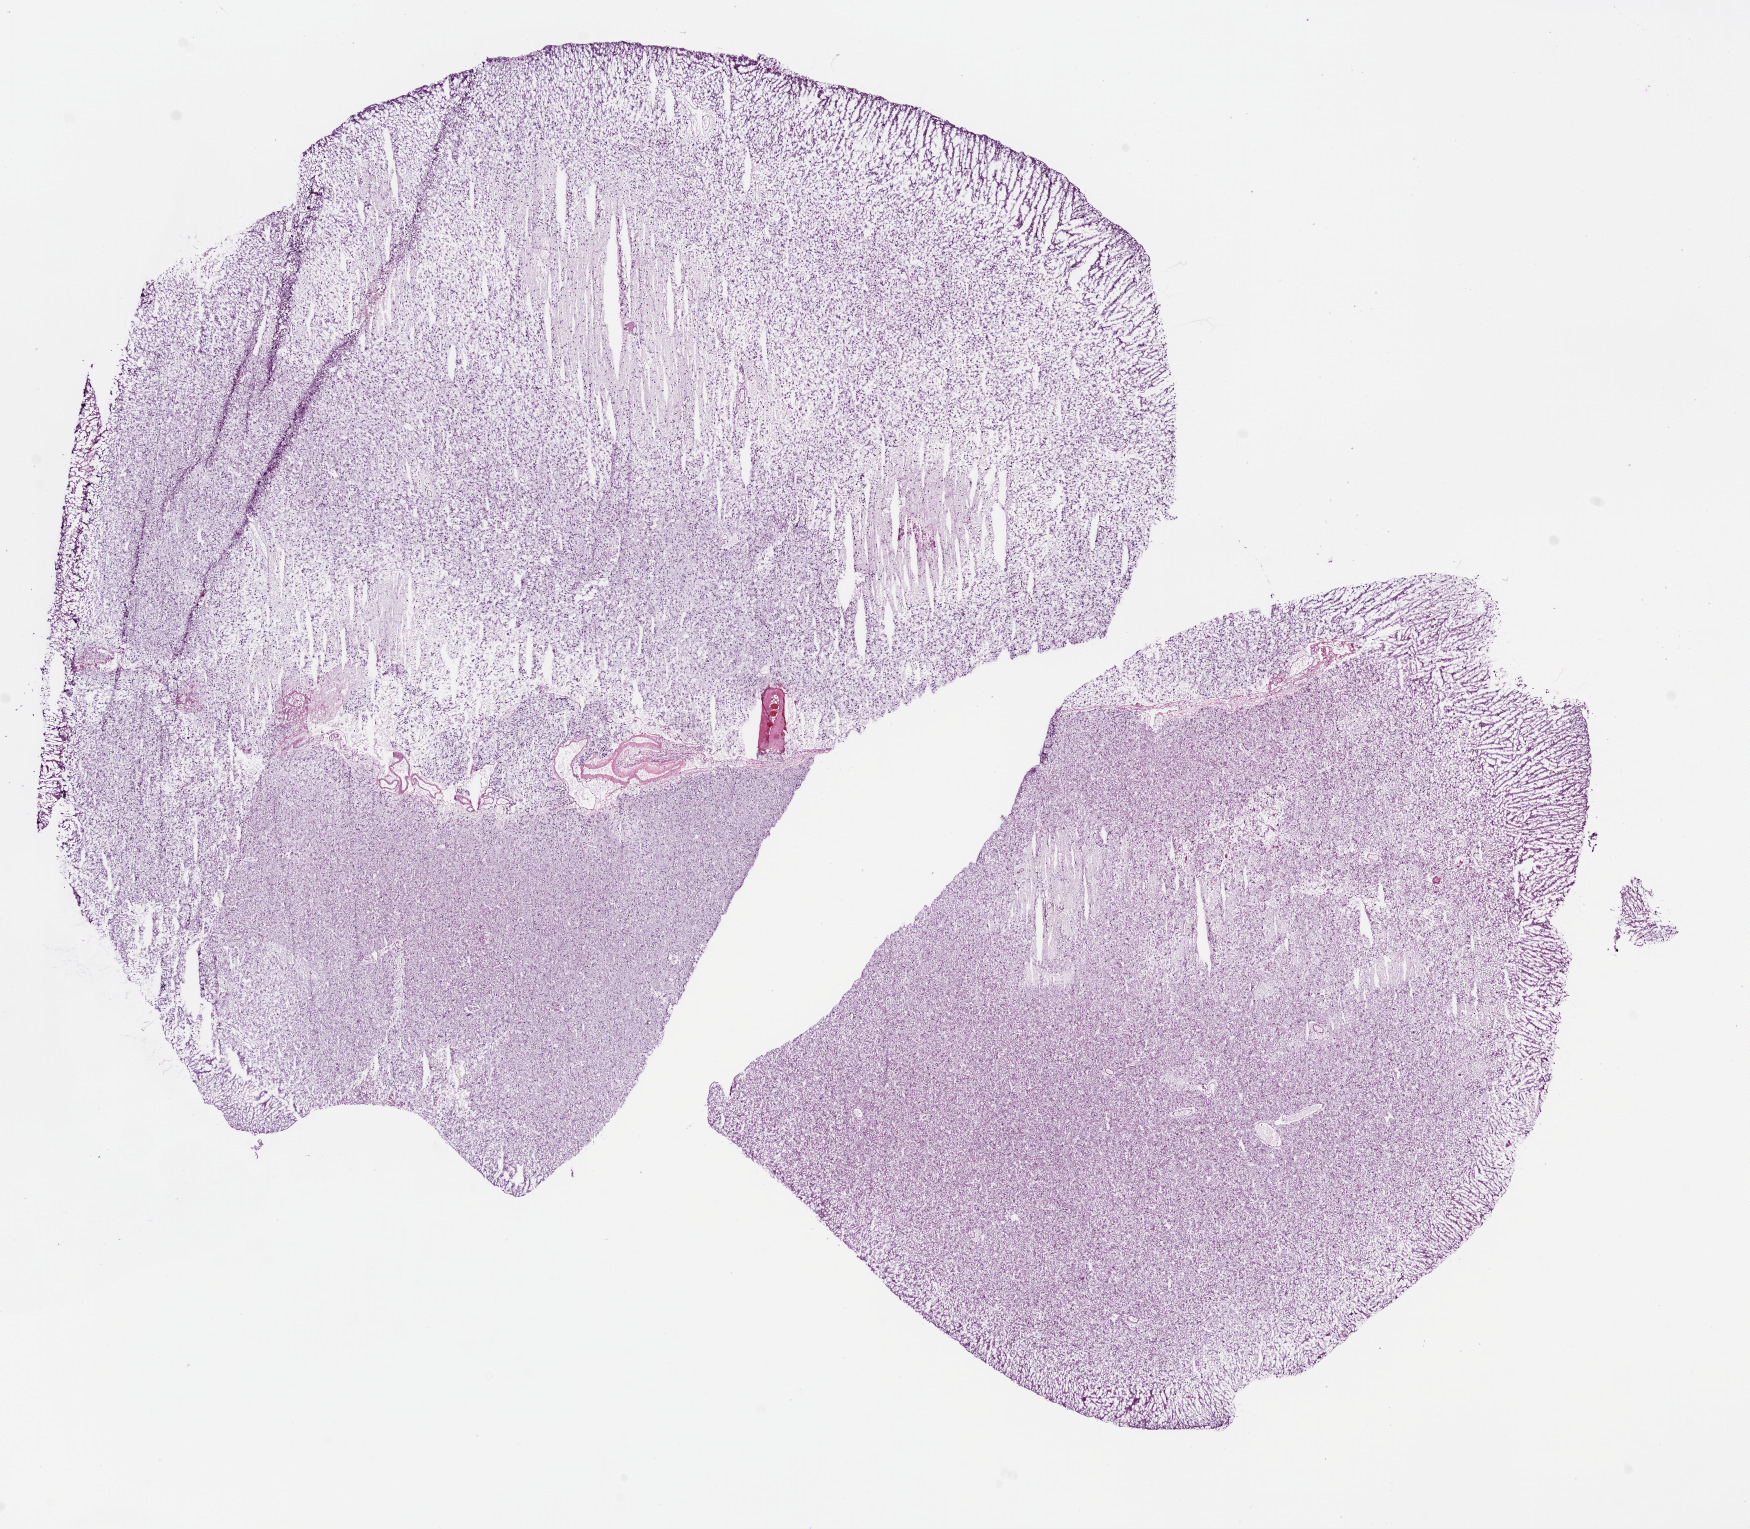
Whole-slide histology image, Hematoxylin and eosin (H&E) stained — whole scanned area (about 14.0 x 12.3 mm, from a 20x scan) shown as a low-resolution overview. Frozen section from the bottom of the tissue portion. Primary tumour sample from the brain. Patient: male, age at initial diagnosis 31 years. Histologic grade: G3 (poorly differentiated). Slide review estimates, as recorded: tumour cells 95%, tumour nuclei 70%, normal cells 0%, stromal cells 5%, necrosis 0%.
Laterality: right. Pathologic diagnosis: Oligodendroglioma, anaplastic.